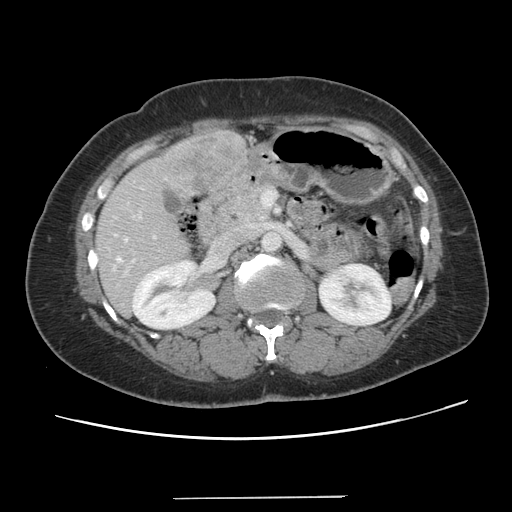
Contrast-enhanced abdominal CT, one axial slice; position 57 of 141 along the scan axis; 120 kVp; soft-tissue window (W 400 / L 40 HU); 2.5 mm slice thickness; 512 × 512 image matrix, field of view 366 × 366 mm. Female patient, age 53 years. Case-level facts recorded for this patient, not image findings: diagnosis: colorectal cancer liver metastases, imaged before liver resection; multiple liver metastases: no; largest metastasis: 14.5 cm; disease in both lobes: yes.
Annotated regions visible in this slice (outlined manually by an expert reader):
- hepatic veins: box from (x=116, y=238) to (x=126, y=261) px
- liver: (x=96, y=129)–(x=247, y=315)
- planned liver remnant (the part of the liver to remain after resection): (x=96, y=216)–(x=188, y=315)
- portal vein (with intrahepatic branches): (x=139, y=217)–(x=154, y=237)
- liver metastasis: (x=175, y=134)–(x=241, y=190)